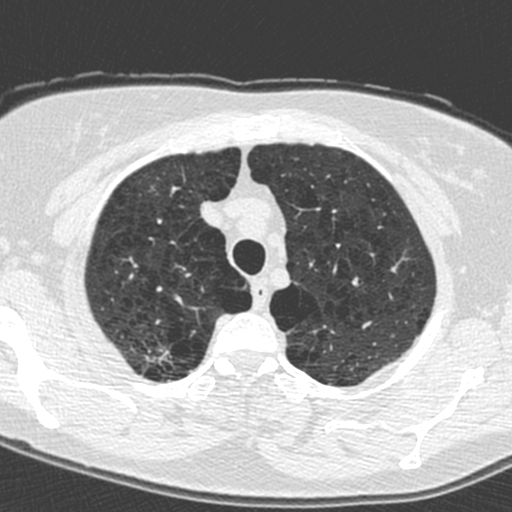
Low-dose screening chest CT, axial slice, baseline annual screen, lung window (W 1500 / L -600 HU), slice 24 of 224 in the series, 512 × 512 image matrix, field of view 278 × 278 mm. Female participant, aged 59 years at enrolment.
Expert reader's lesion annotation, bounding box [x1, y1, x2, y2] px = [131, 337, 177, 376]. No non-calcified nodule or mass ≥4 mm was recorded by the screening reader at this exam. Later outcome: lung cancer diagnosed 881 days after this screen — adenocarcinoma, NOS, right upper lobe, poorly differentiated (G3), stage IA (AJCC 6th edition), 20 mm at pathology.